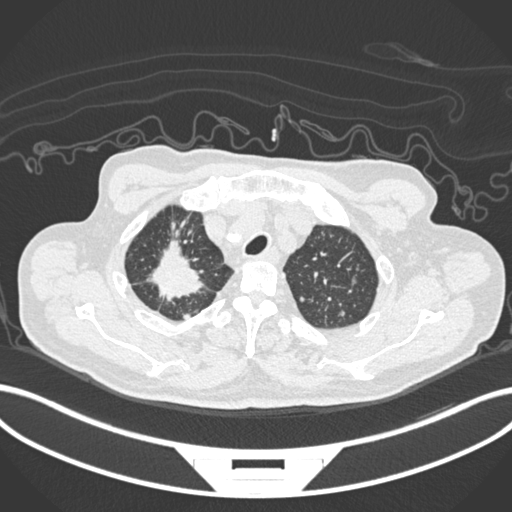
Chest CT, one axial slice; slice 187 of 207 in the series (ordered by position); 120 kVp; lung window (W 1500 / L -600 HU); 1 mm slice thickness; 512 × 512 image matrix. Male patient, age 69 years. Case-level facts recorded for this patient, not image findings: clinical TNM (as recorded): T1c N1 M1.
Outlined on this slice (rectangle marked by the reading radiologist):
- lung tumour (recorded histology: adenocarcinoma): bounding box <150,237,206,303> (left, top, right, bottom; pixels)